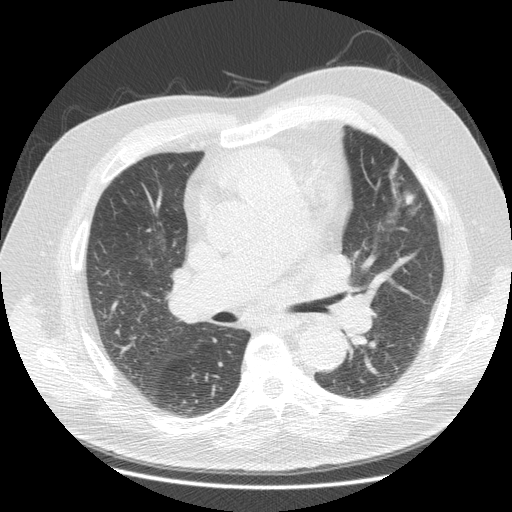
Low-dose screening chest CT, one axial slice. Slice 61 of 116 in the series (ordered by position). Reconstruction kernel STANDARD. 140 kVp. Lung window (W 1500 / L -600 HU). 512 × 512 image matrix, field of view 390 × 390 mm.
Structures marked on this image (manually delineated by an expert):
- lesion 1 (tumor, upper lobe of left lung): bounding box (x1, y1, x2, y2) in pixels: (404, 192, 415, 205)